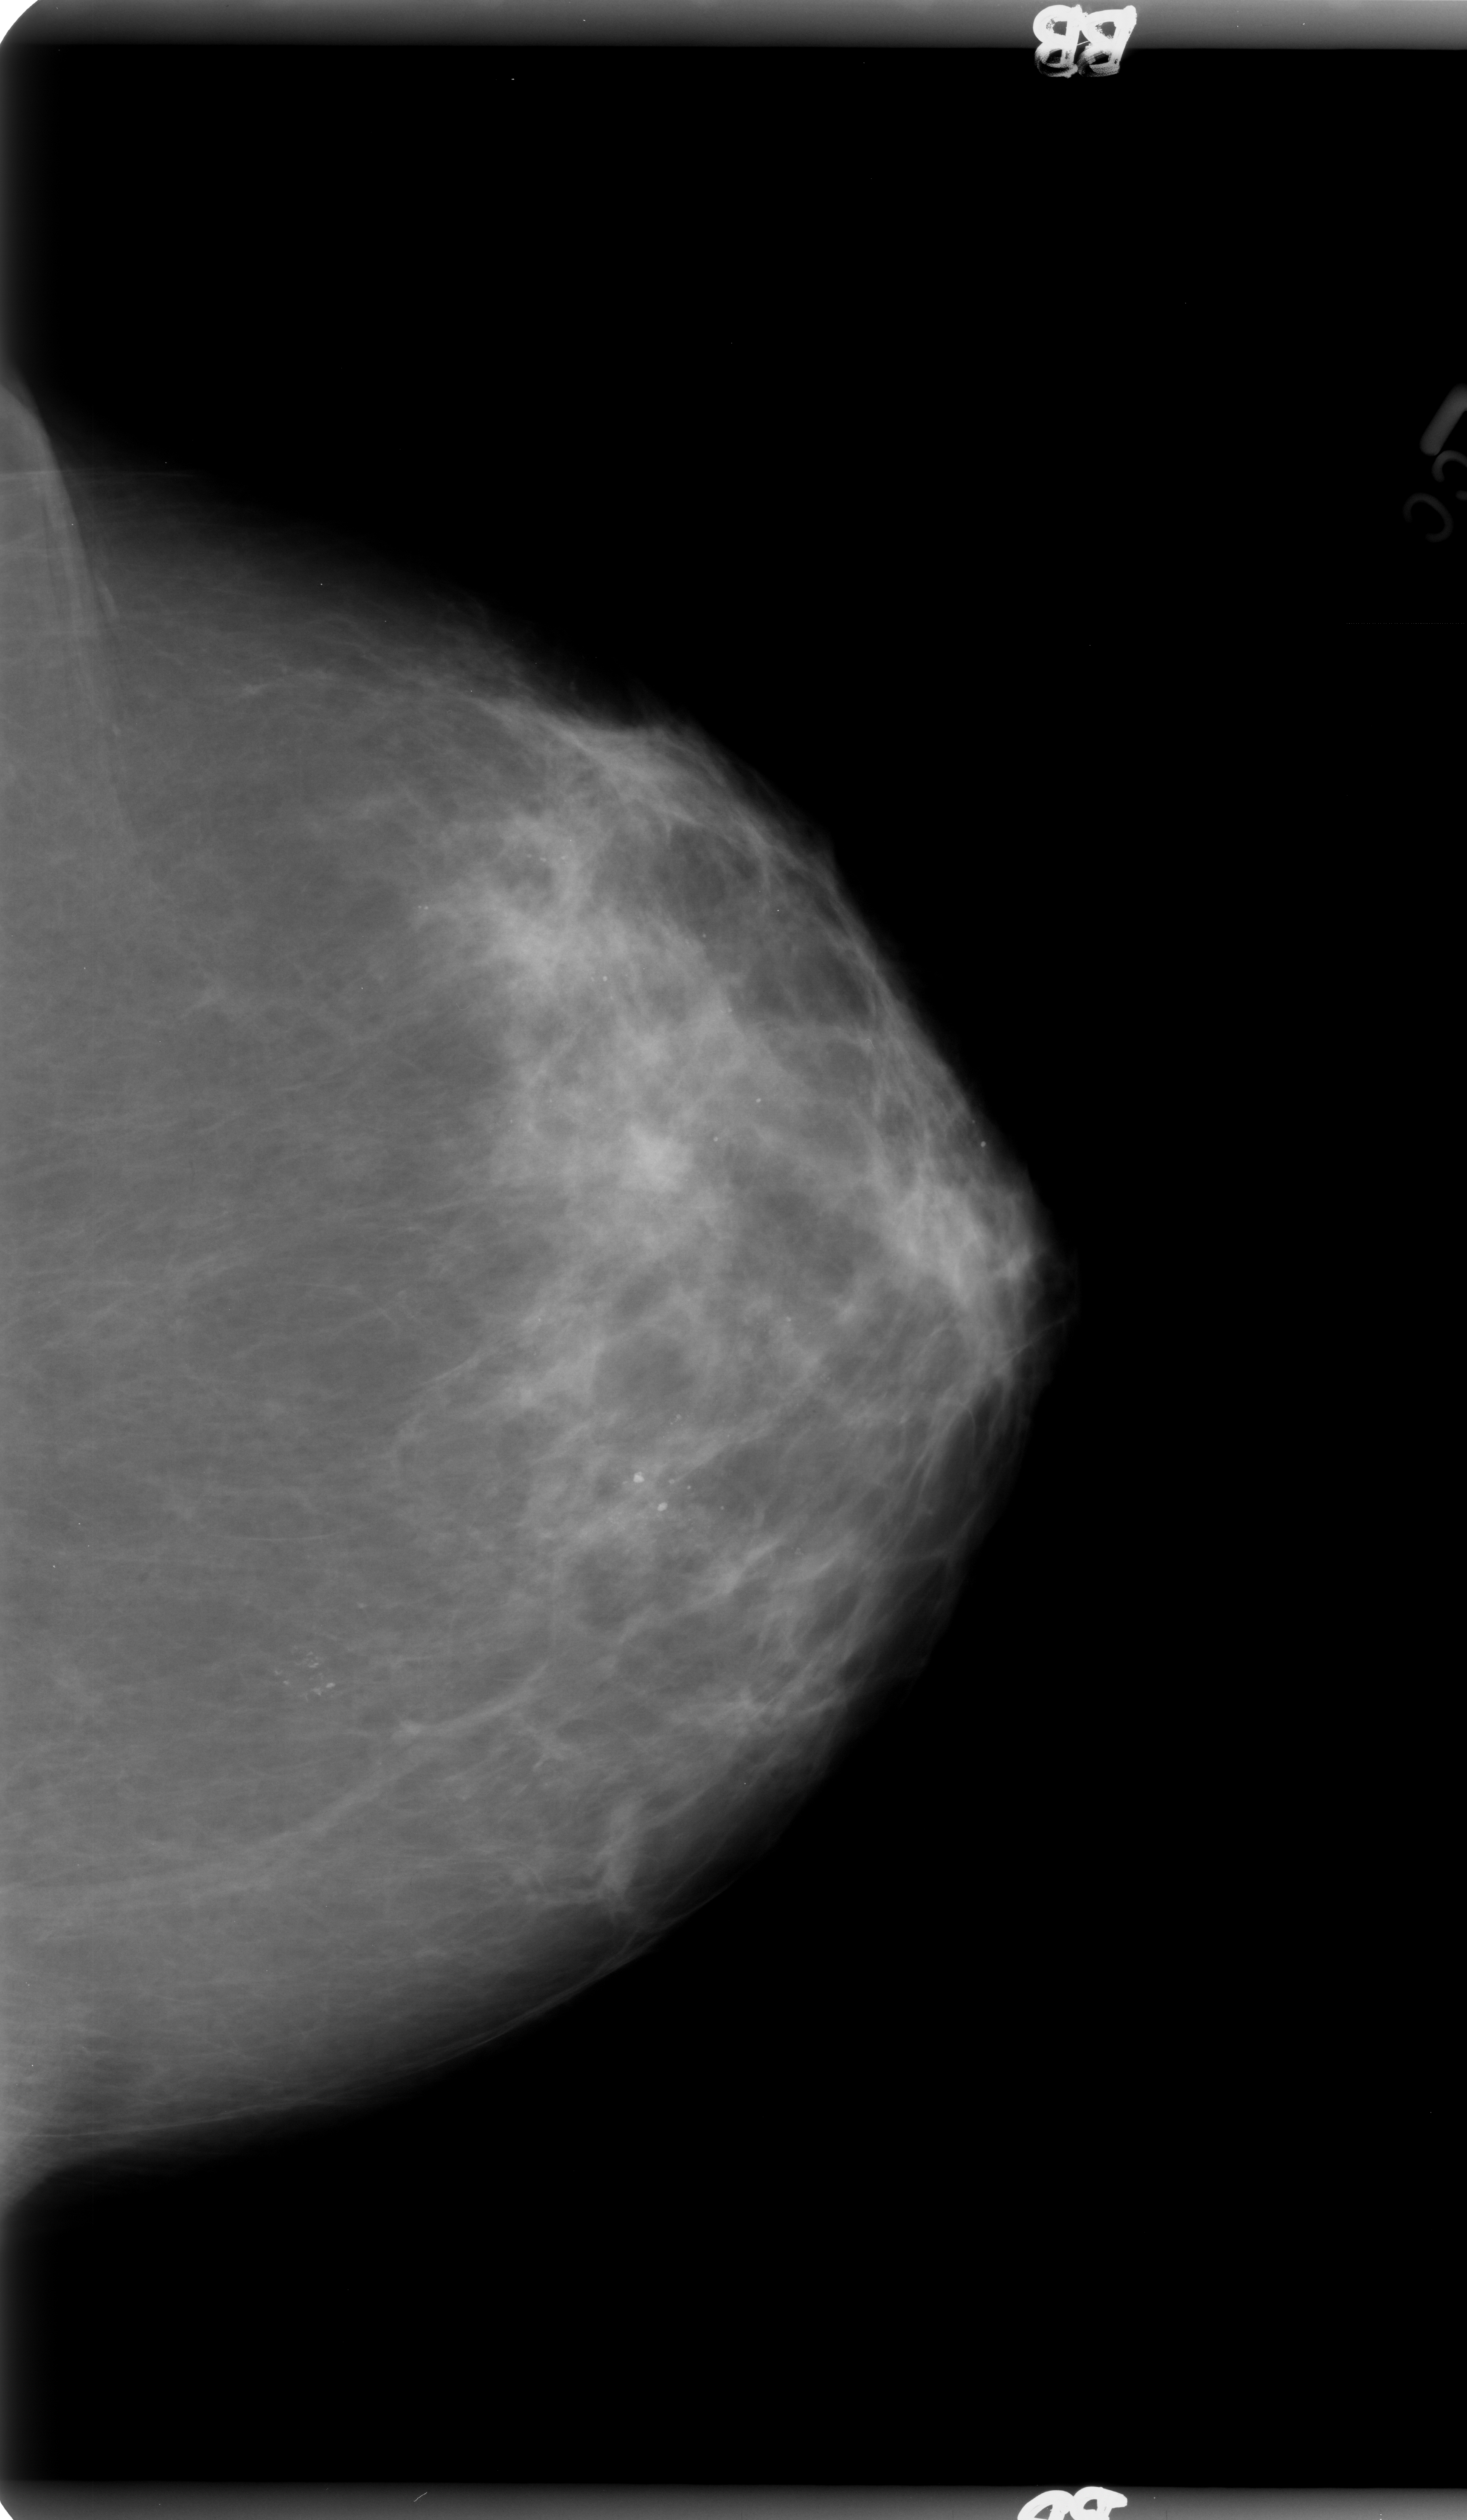
Mammogram (digitized film), left breast, CC view, breast composition: scattered fibroglandular densities (BI-RADS density category 2 of 4).
Marked findings (only marked abnormalities are described; nothing is implied about the rest of the image): calcifications, morphology pleomorphic, distribution clustered; BI-RADS assessment category 4; subtlety rating 3 on a 1 (subtle) to 5 (obvious) scale; pathology (as recorded): benign.